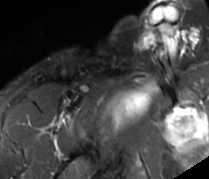
MRI of an extremity soft-tissue mass, one axial slice; slice 76 of 89 in the series (ordered by position); STIR; MR volume resampled by the dataset authors to the PET/CT grid (not the native acquisition matrix); 3.27 mm slice thickness; 209 × 179 image matrix, field of view 204 × 175 mm. Male patient. Case-level facts recorded for this patient, not image findings: histological type: undifferentiated - pleiomorphic; grade: high; site of the primary tumour: right thigh.
Annotated regions visible in this slice (expert contour drawn on MRI and transferred to this co-registered scan by the dataset authors):
- gross tumour volume including surrounding oedema: bounding box (x1, y1, x2, y2) in pixels: (105, 80, 159, 133)
- gross tumour volume (mass): (108, 89, 149, 127)